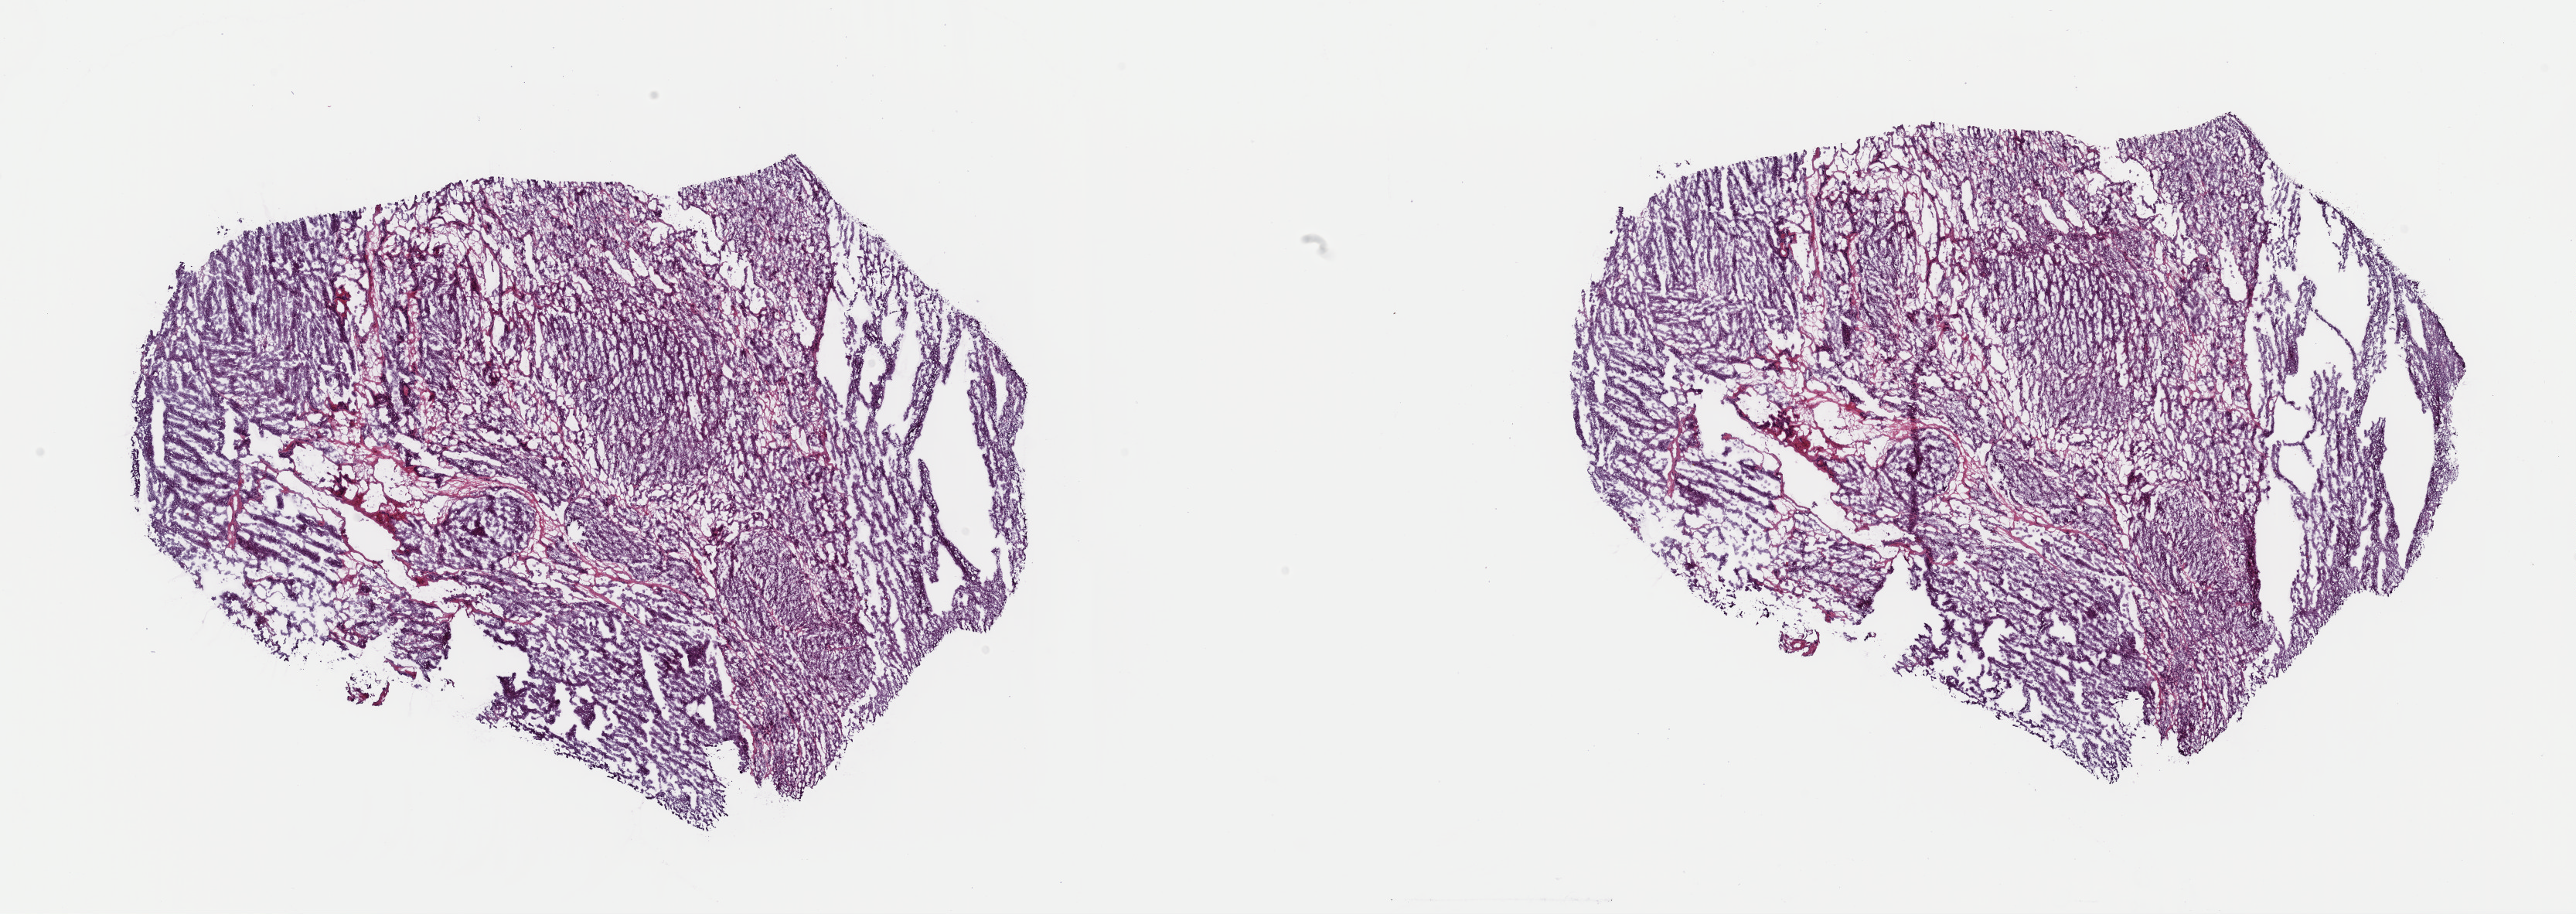
Hematoxylin and eosin (H&E) stained whole-slide image — shown as a low-resolution overview of the whole scanned area (about 26.3 x 9.3 mm, acquisition: 40x scan). Frozen section from the top of the tissue portion. Adrenal cortex, primary tumour sample. Patient: female, age at initial diagnosis 45 years. Pathologist review of this section (percent, as recorded): tumour cells 95%, tumour nuclei 90%, normal cells 0%, stromal cells 5%, necrosis 0%. Inflammatory infiltration, as recorded: lymphocyte infiltration 5%, monocyte infiltration 0%, neutrophil infiltration 0%.
Pathologic diagnosis: Adrenal cortical carcinoma. Lymph nodes positive (case pathology): 0 of 2 examined.